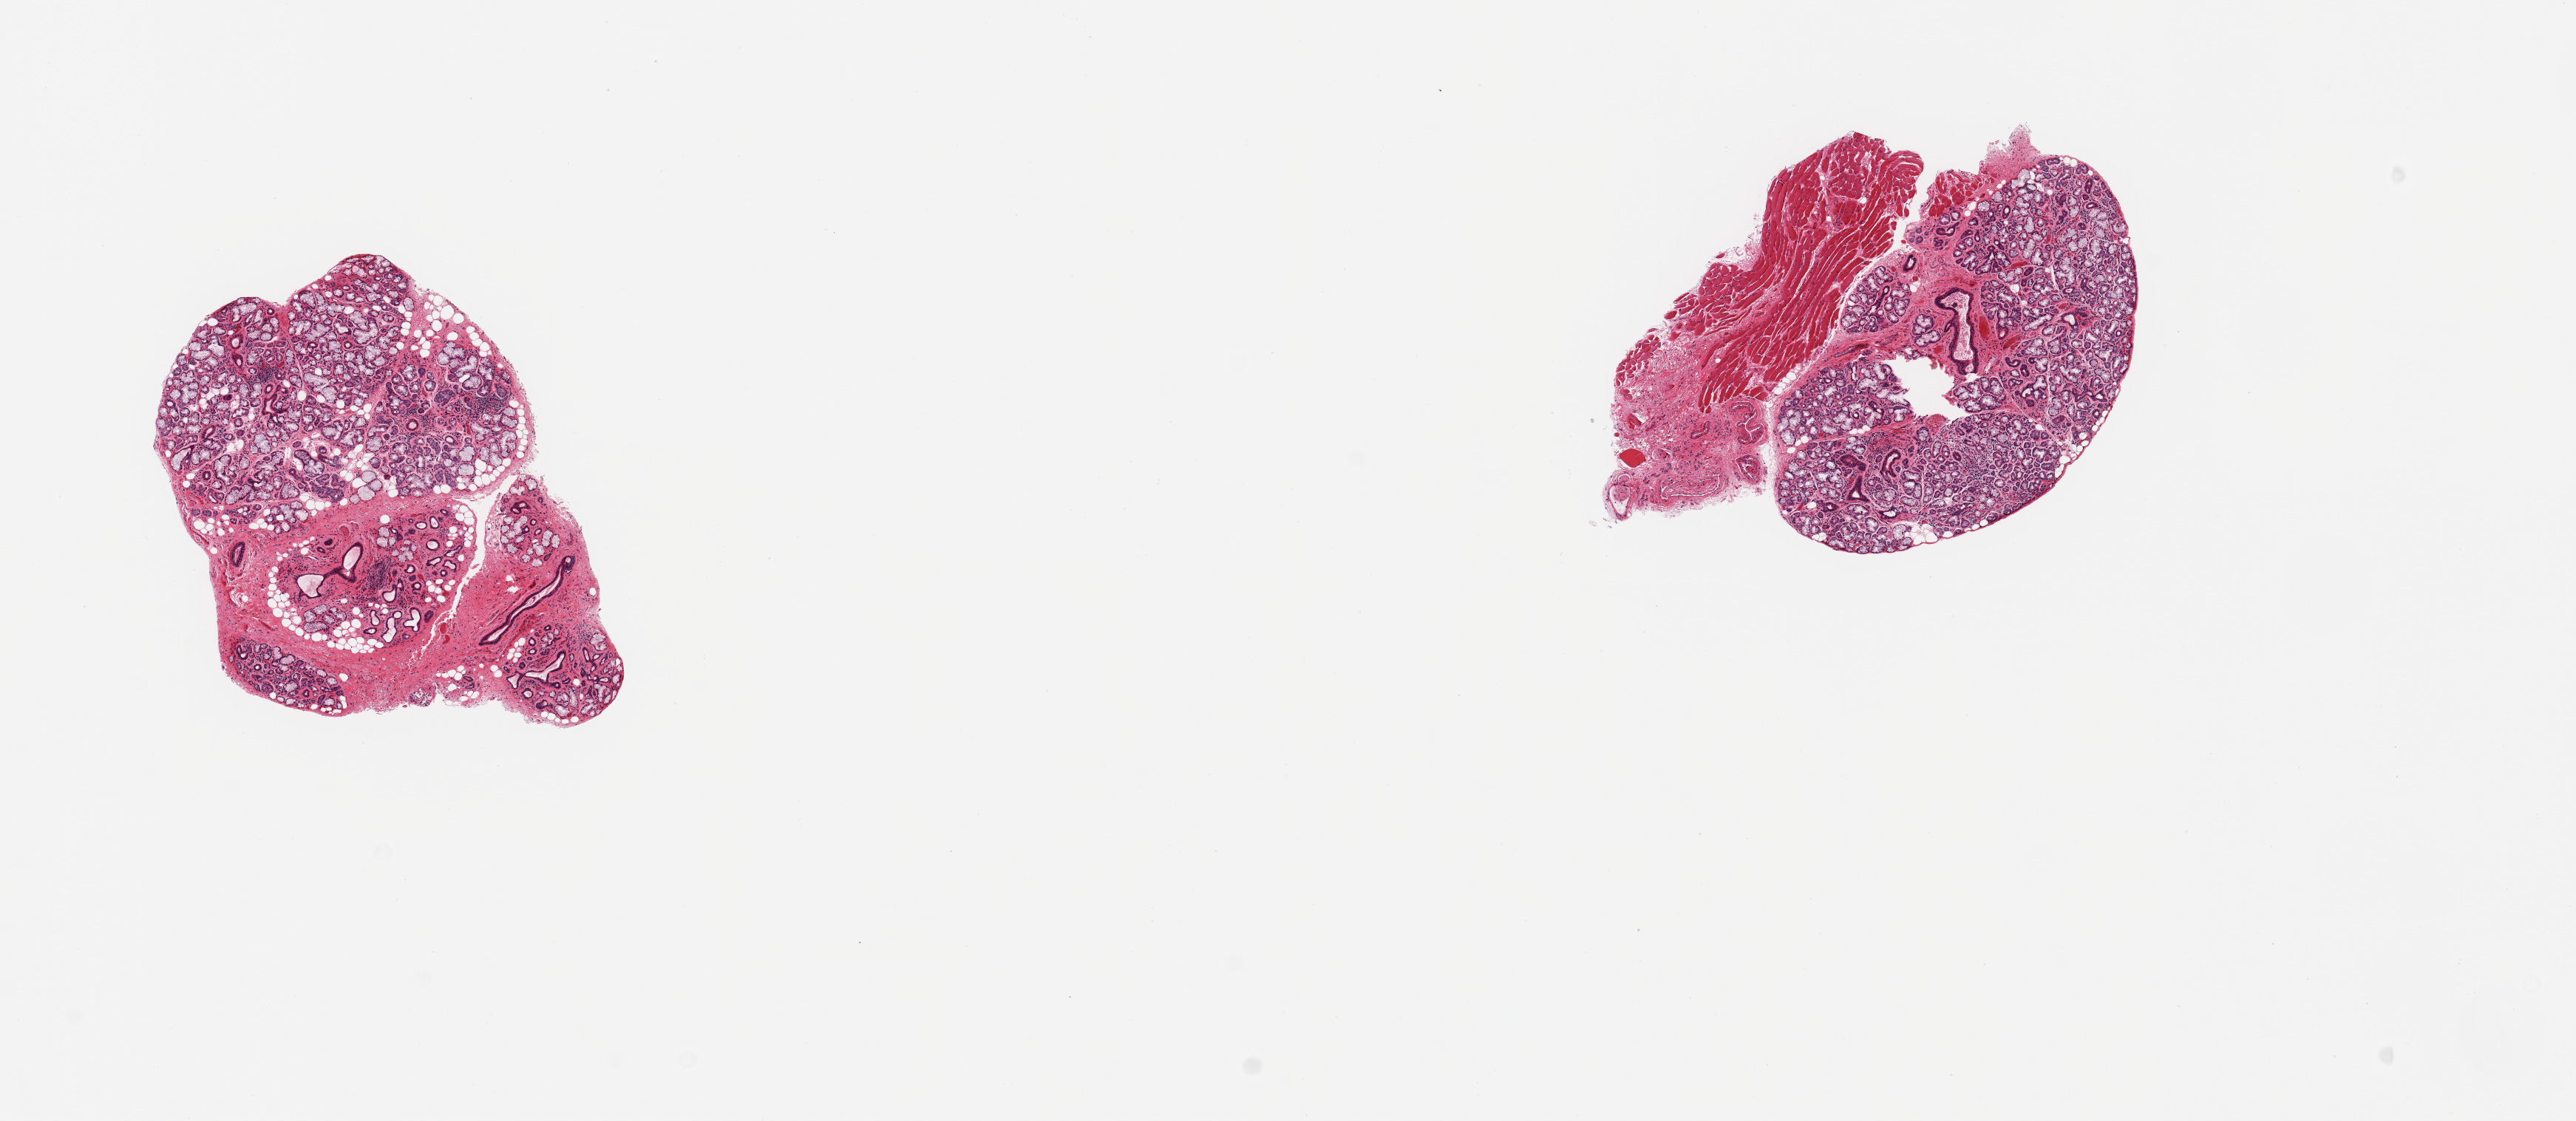
Haematoxylin and eosin whole-slide image, brightfield — a low-resolution overview of the entire scanned area, about 13.8 x 6.0 mm (acquisition: 20x scan), PAXgene-fixed, paraffin-embedded tissue, section of minor salivary gland (target tissue), tissue donor sample.
- reviewer comment on this tissue sample: 2 pieces, ~60% glandular elements; rest is muscle/fibrous tissue